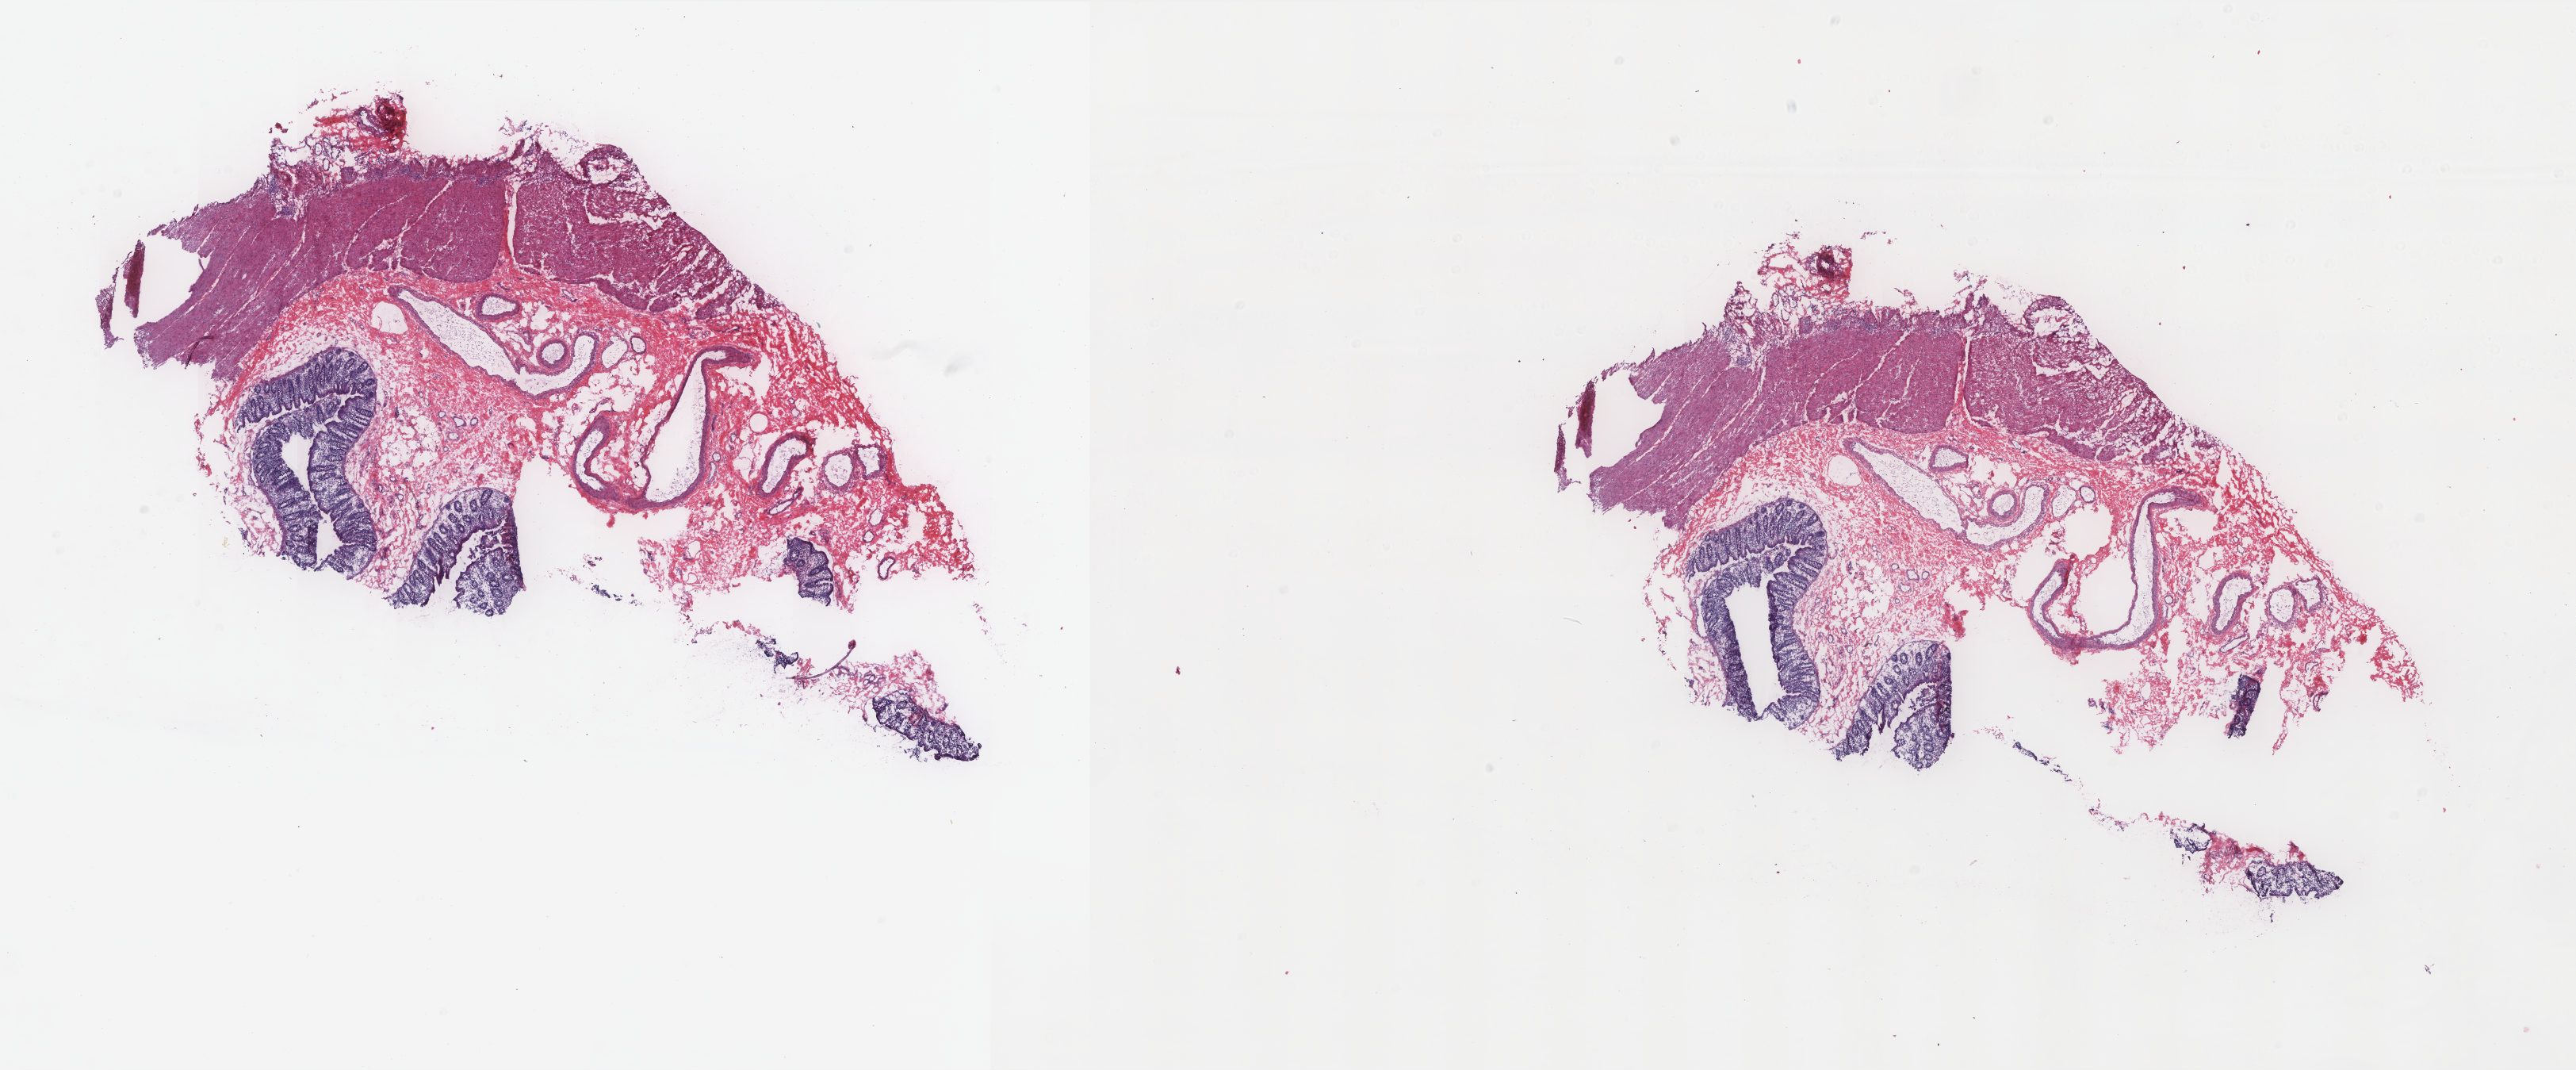
Digitized Hematoxylin and eosin (H&E) stained tissue section (whole slide) — a low-resolution overview of the entire scanned area, about 25.9 x 10.8 mm. Frozen section. Colon, solid tissue normal (non-tumour tissue) sample. Male patient; age at initial diagnosis 59 years. Pathologist review of this section (percent, as recorded): tumour cells 0%, normal cells 100%. Inflammatory infiltration, as recorded: lymphocyte infiltration 25%, monocyte infiltration 5%, neutrophil infiltration 0%.
* this section: solid tissue normal (non-tumour) sample from the same patient
* patient diagnosis: Adenocarcinoma, NOS (cecum)